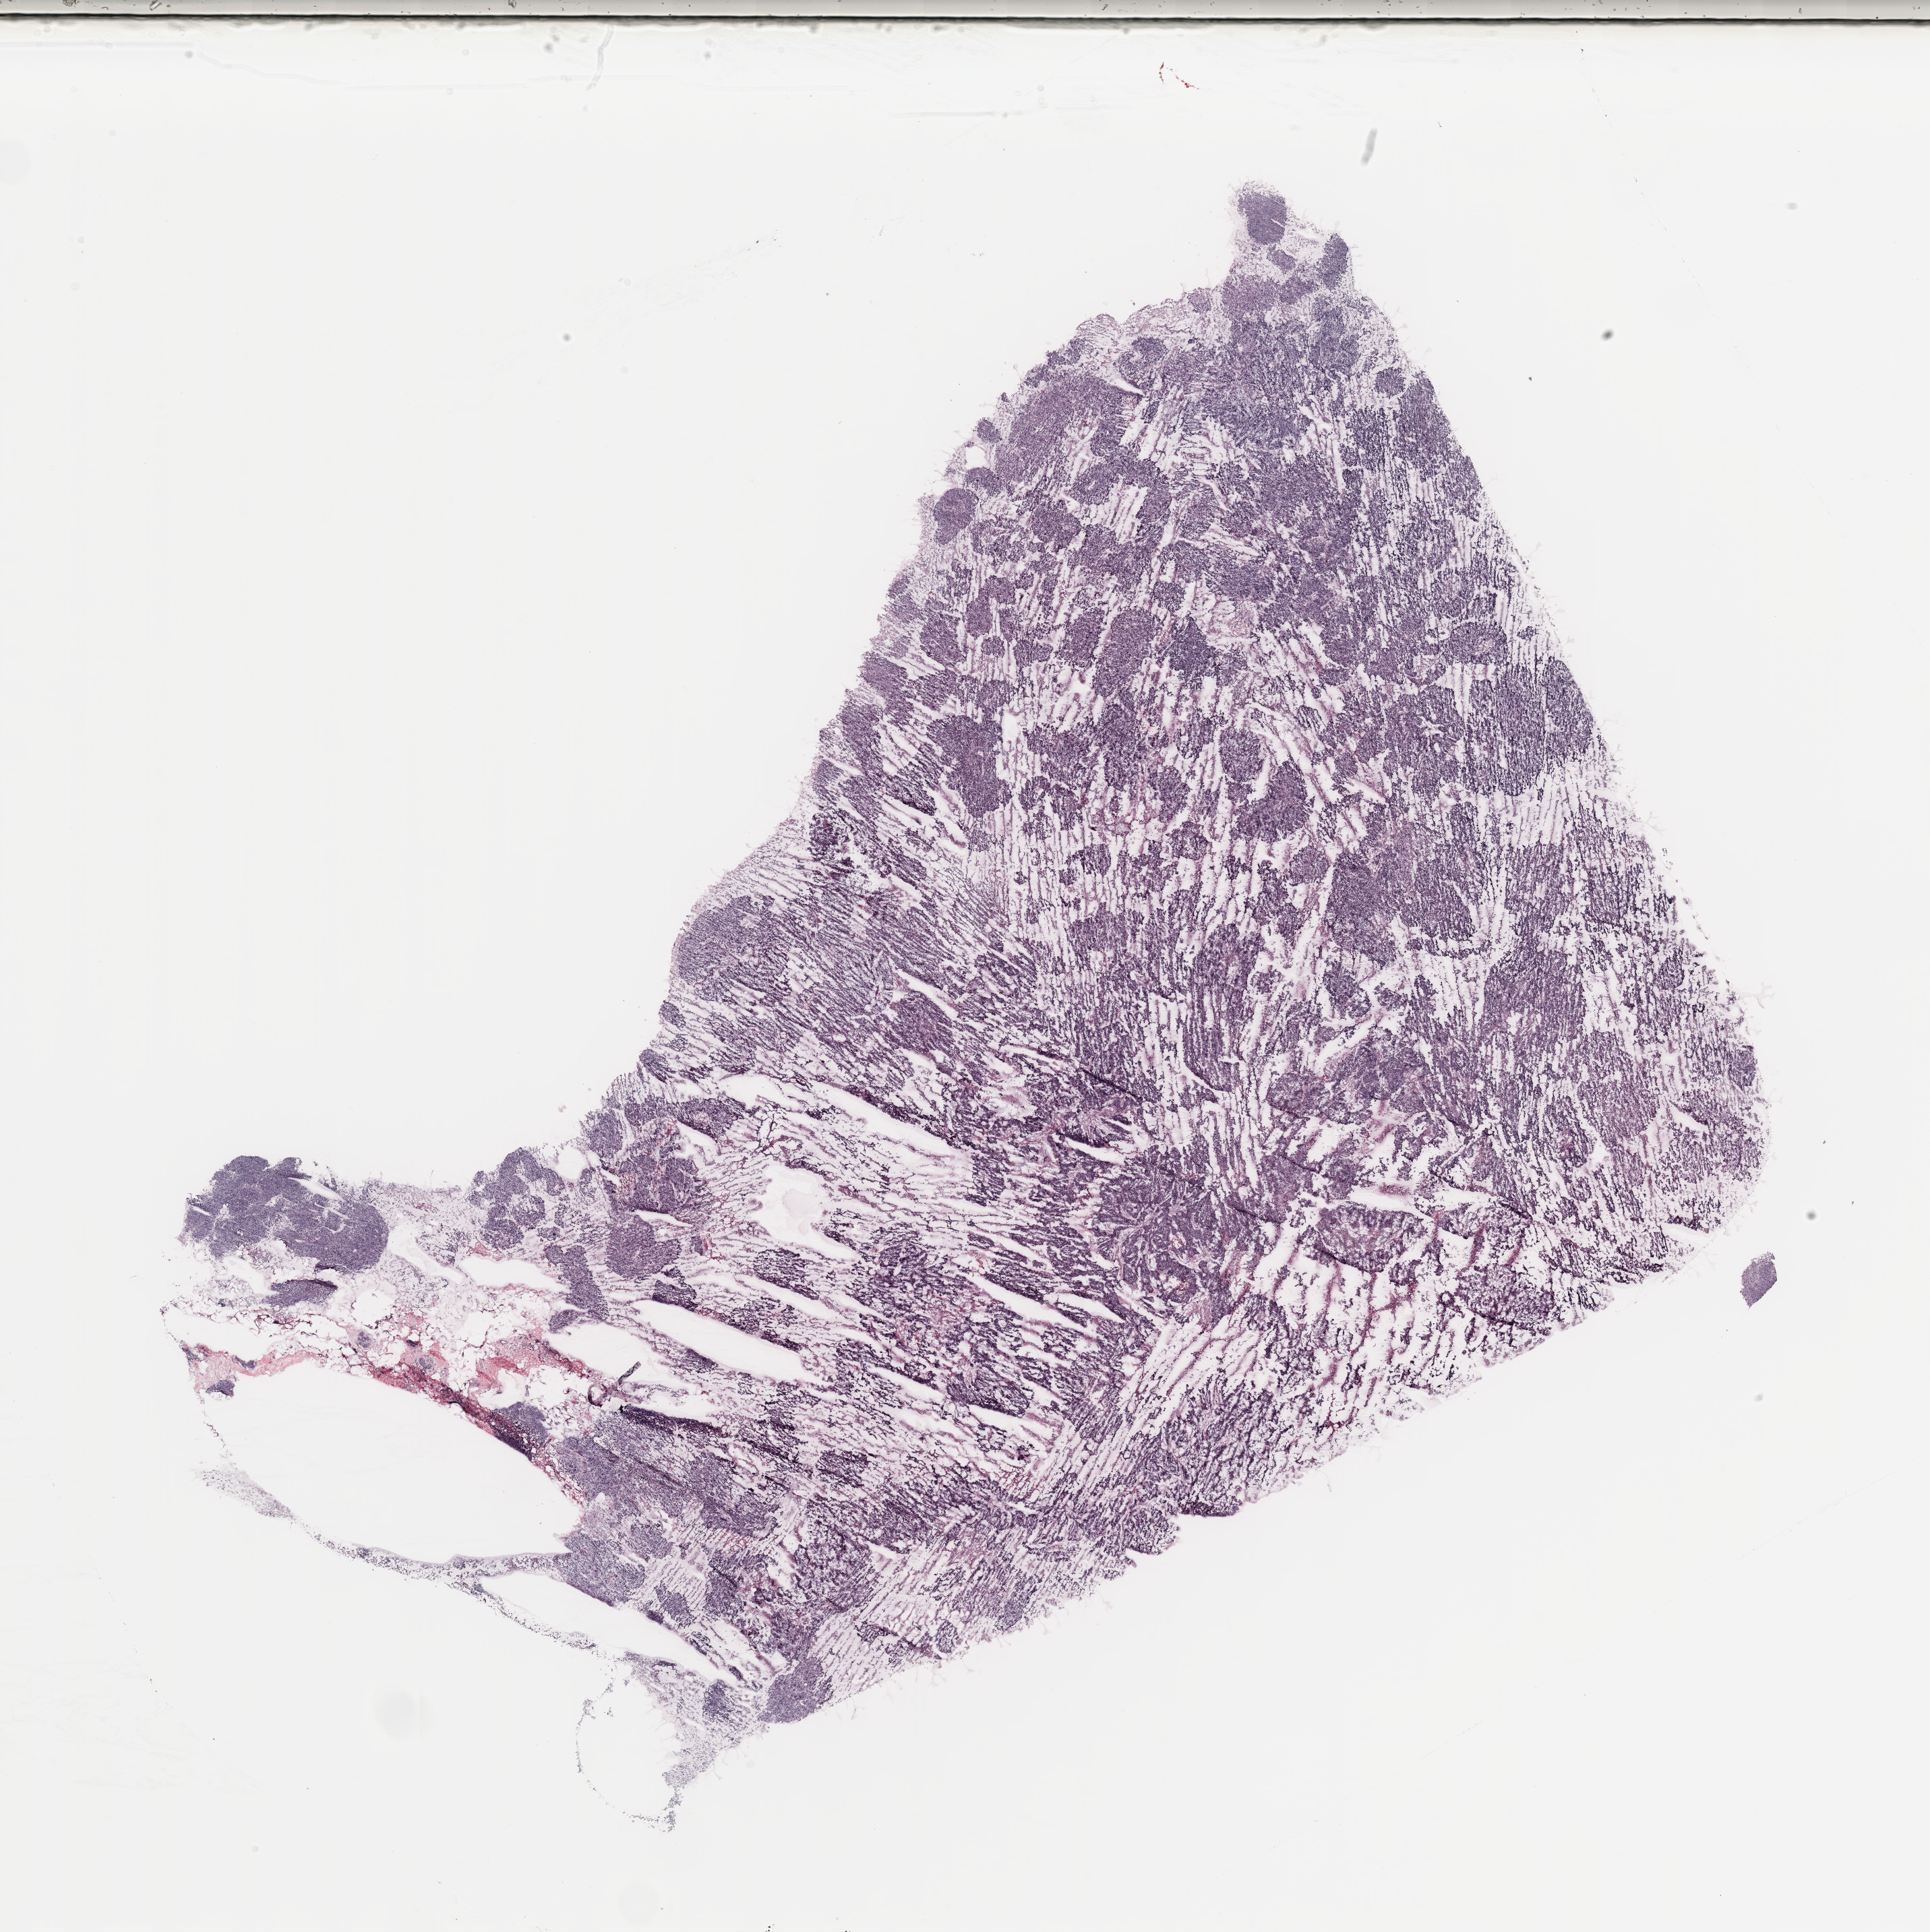
H&E whole-slide image — shown as a low-resolution overview of the whole scanned area (about 22.6 x 22.7 mm), breast, tumour tissue. Patient: female, age 66 years.
* AJCC pathologic stage: IIIA
* diagnosis: Infiltrating duct carcinoma, NOS